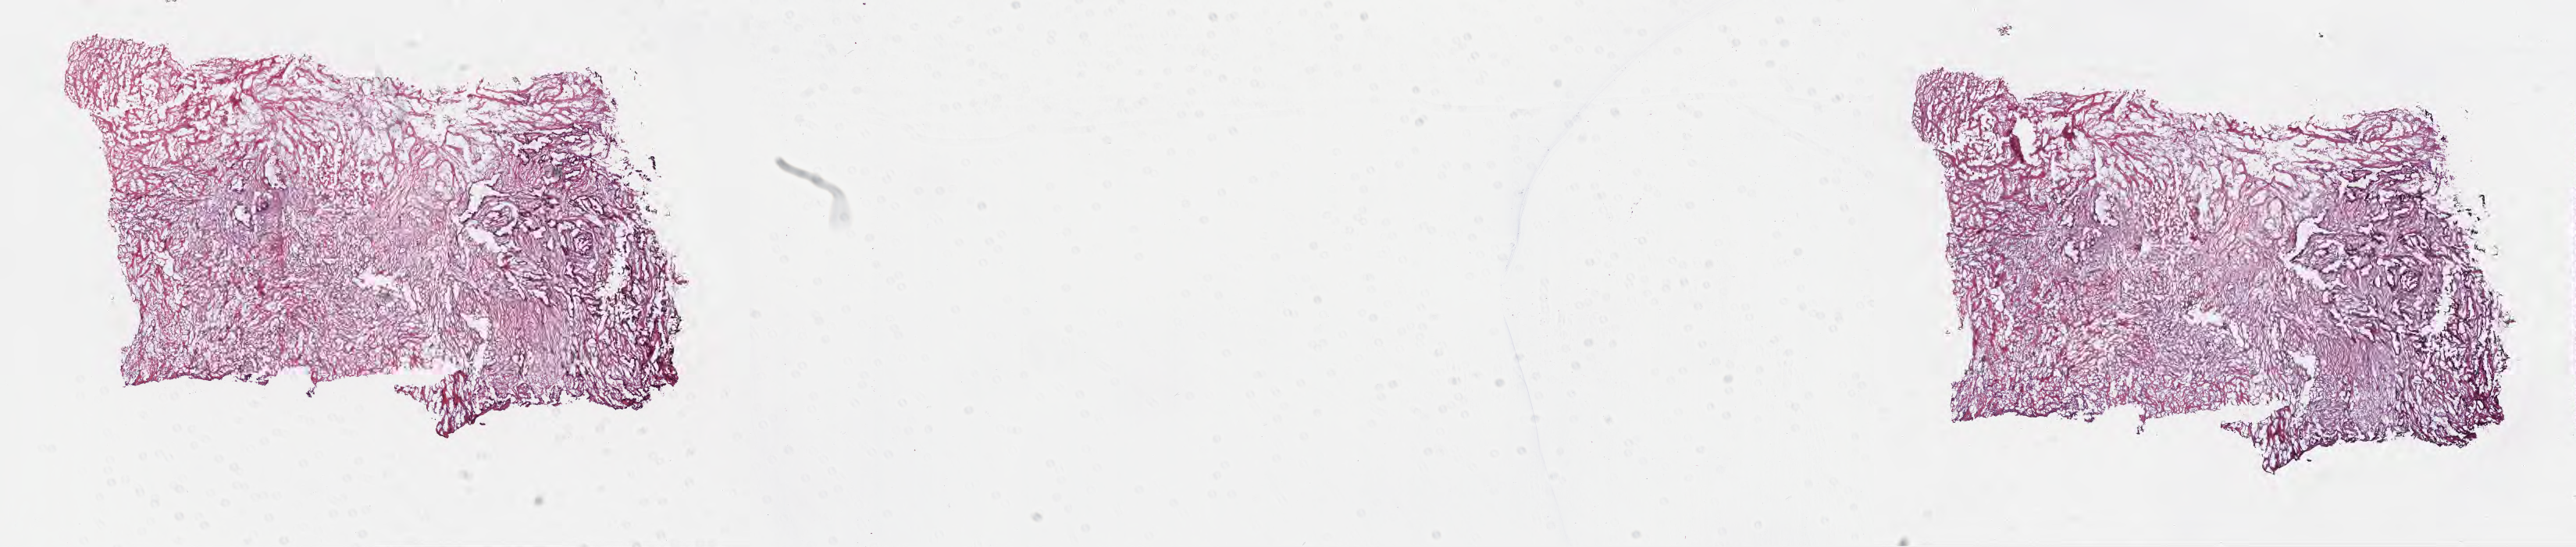
Digitized haematoxylin and eosin-stained section — shown as a low-resolution overview of the whole scanned area (about 26.7 x 5.7 mm). Frozen section. Specimen: primary tumor. Site: body of pancreas. Male patient; age at initial diagnosis 79 years.
Histologic diagnosis: Infiltrating duct carcinoma, NOS.